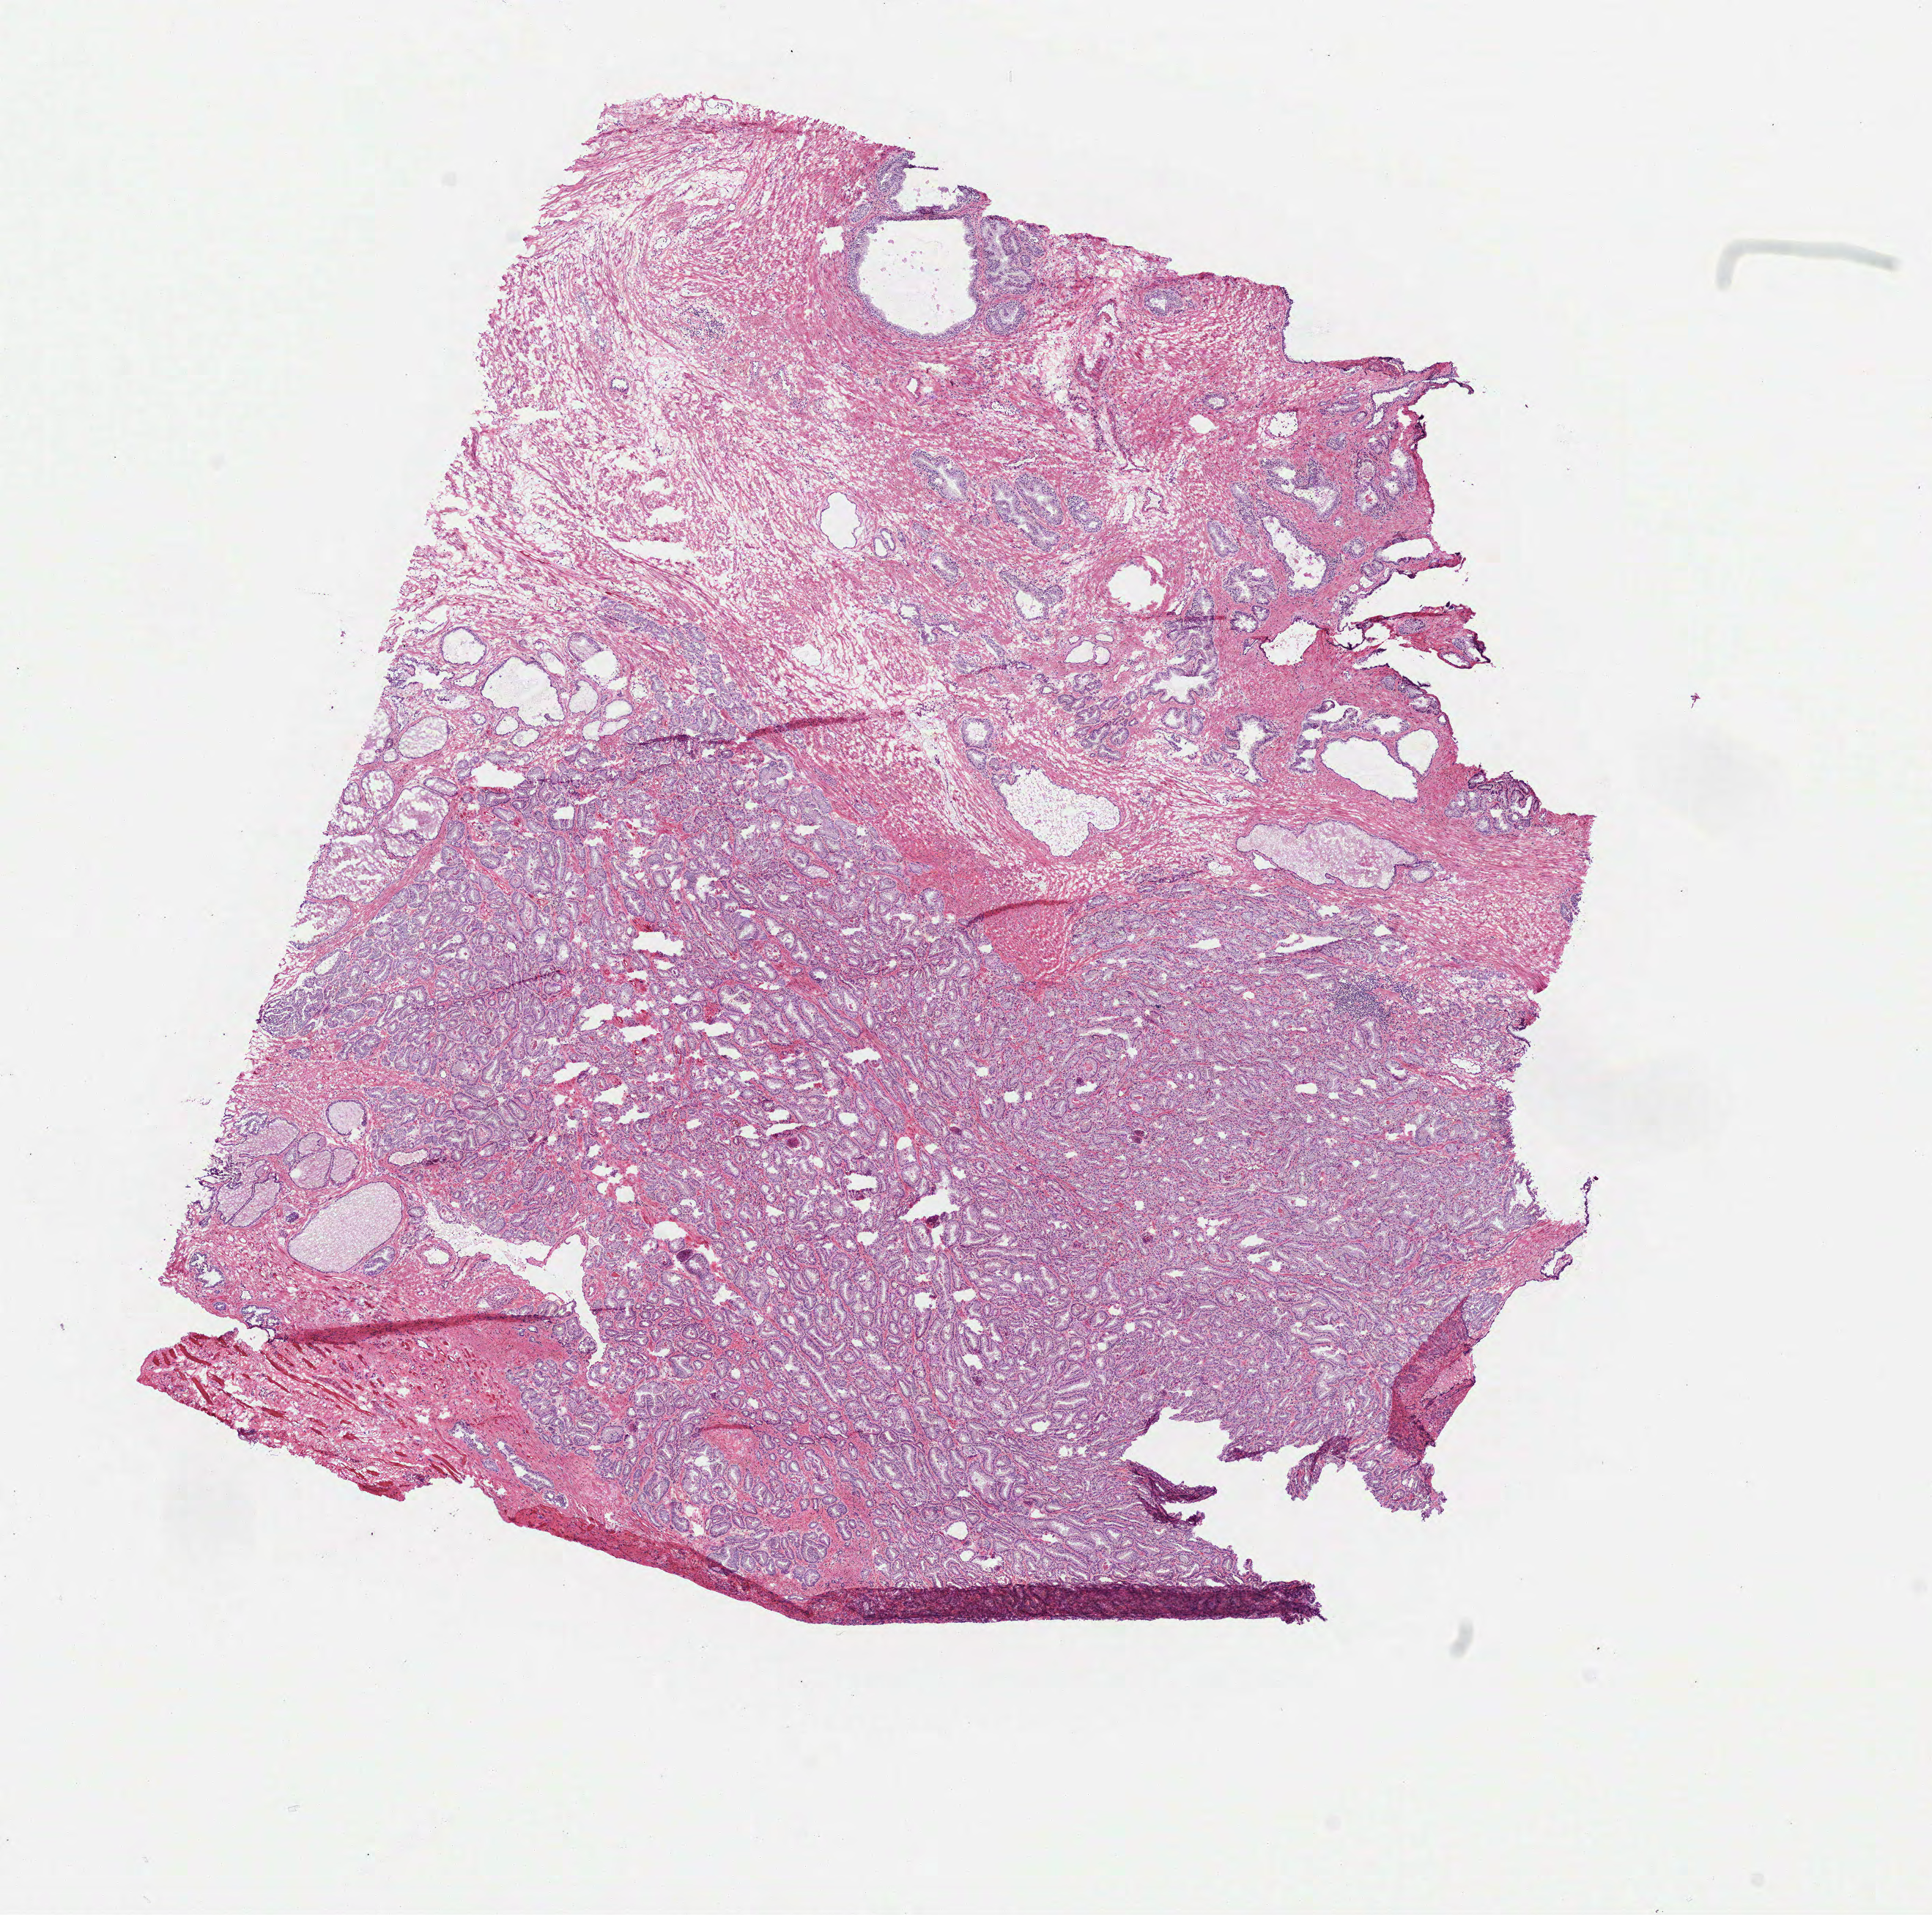
Whole-slide histology image, H&E, a low-resolution overview of the entire scanned area, about 10.6 x 10.5 mm (acquisition: 40x scan), frozen section, sample: primary tumour, prostate. Male patient; age at initial diagnosis 62 years. Gleason score: 7 (3+4). Composition of this section per pathologist review: tumour cells 60%, tumour nuclei 70%, normal cells 5%, stromal cells 35%, necrosis 0%. Infiltration values recorded for this section: lymphocyte infiltration 0%, monocyte infiltration 0%, neutrophil infiltration 0%.
Pathologic diagnosis: Acinar cell carcinoma (prostate gland).